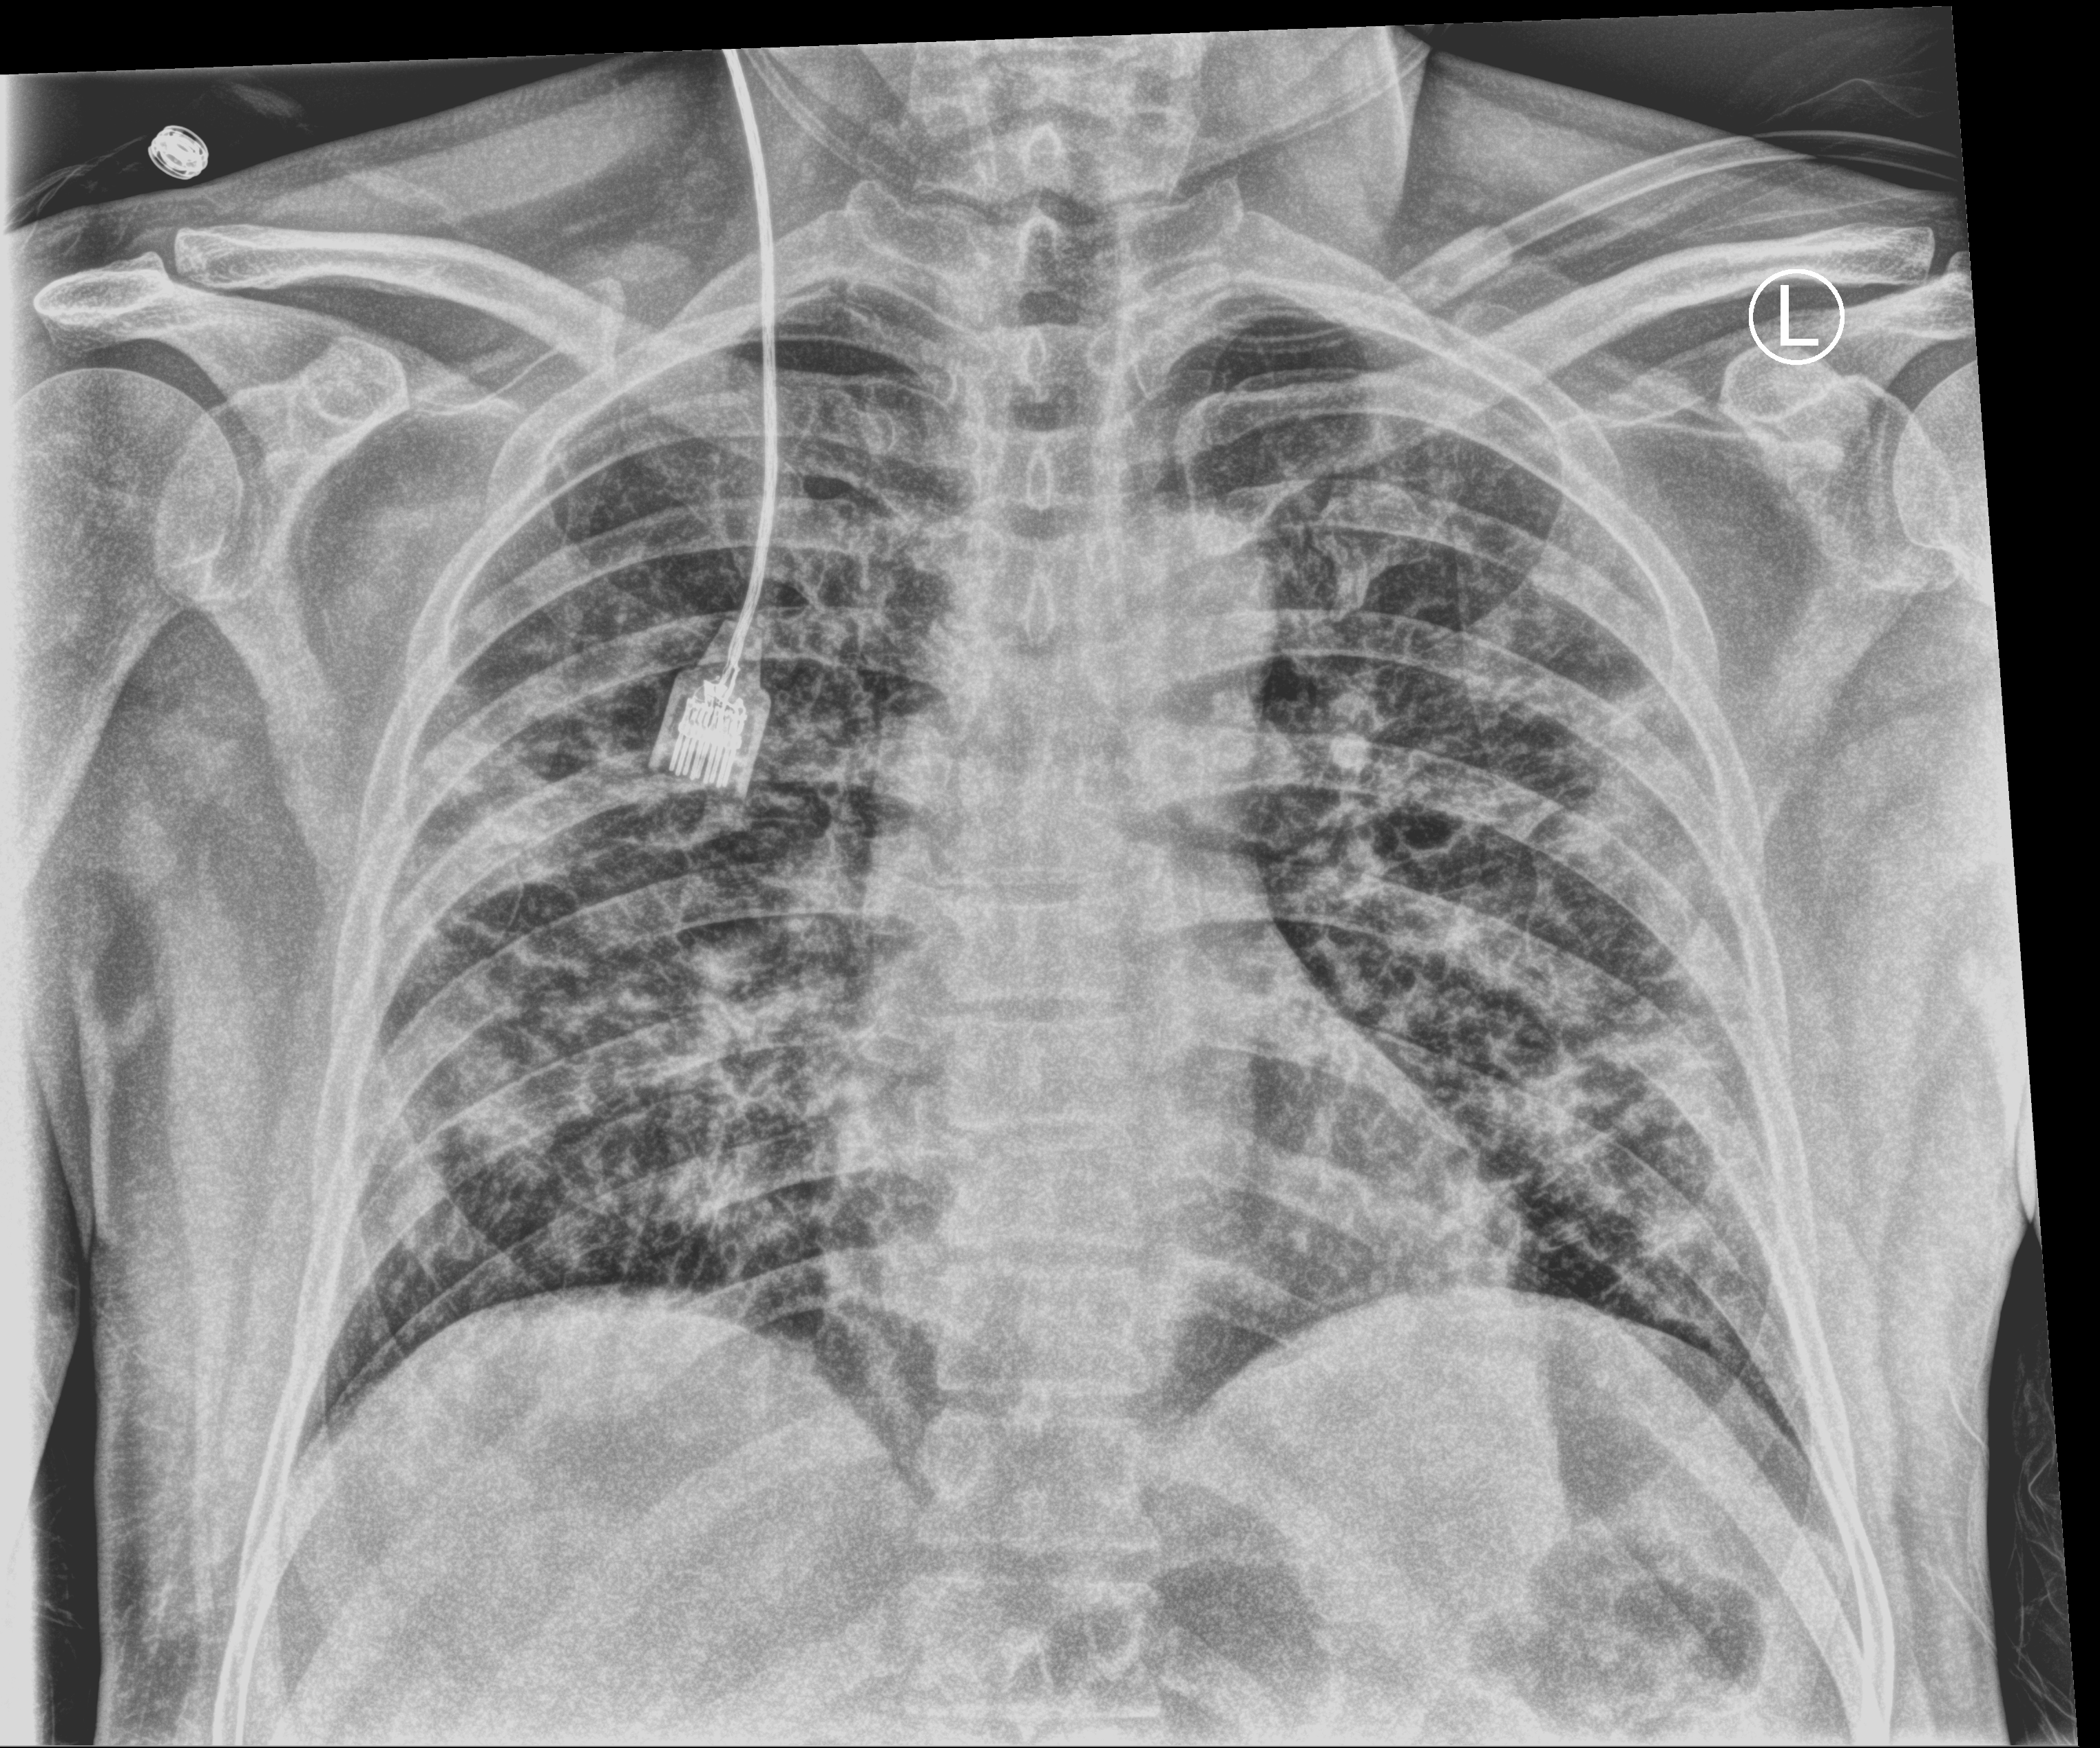
Bedside chest radiograph (computed radiography); anteroposterior (AP) projection. Male patient hospitalised with COVID-19, age 18–59 years.
Hospital-stay facts (about this admission, not read from this image; timing relative to this image not recorded):
- length of hospital stay: 10 days
- hypertension (admission record): no